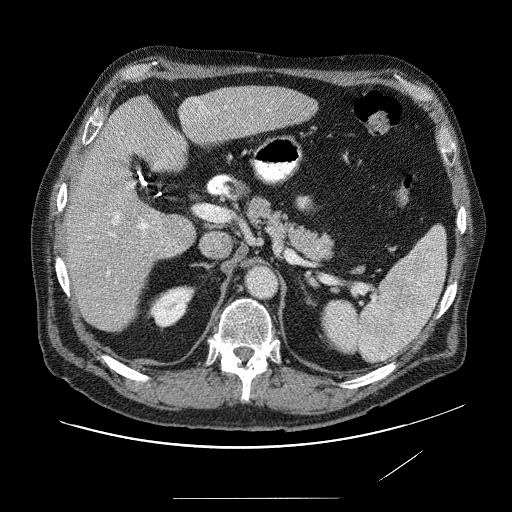
Contrast-enhanced abdominal CT (liver protocol), one axial slice; position 41 of 89 along the scan axis; reconstruction kernel STANDARD; 120 kVp; soft-tissue window (W 400 / L 40 HU); 2.5 mm slice thickness; 512 × 512 image matrix. Case-level facts recorded for this patient, not image findings: diagnosis: hepatocellular carcinoma (patient treated with transarterial chemoembolisation; whether this scan precedes or follows treatment is not stated here); TNM stage (as recorded): Stage-IVA.
Structures marked on this image (semi-automatically segmented with operator editing):
- liver parenchyma outside the tumour (the mass and vessels are separate outlines, so this box may not span the whole liver): bounding box <60,84,322,334> (left, top, right, bottom; pixels)
- mass: <166,237,194,254>
- liver vessels: <98,110,232,292>